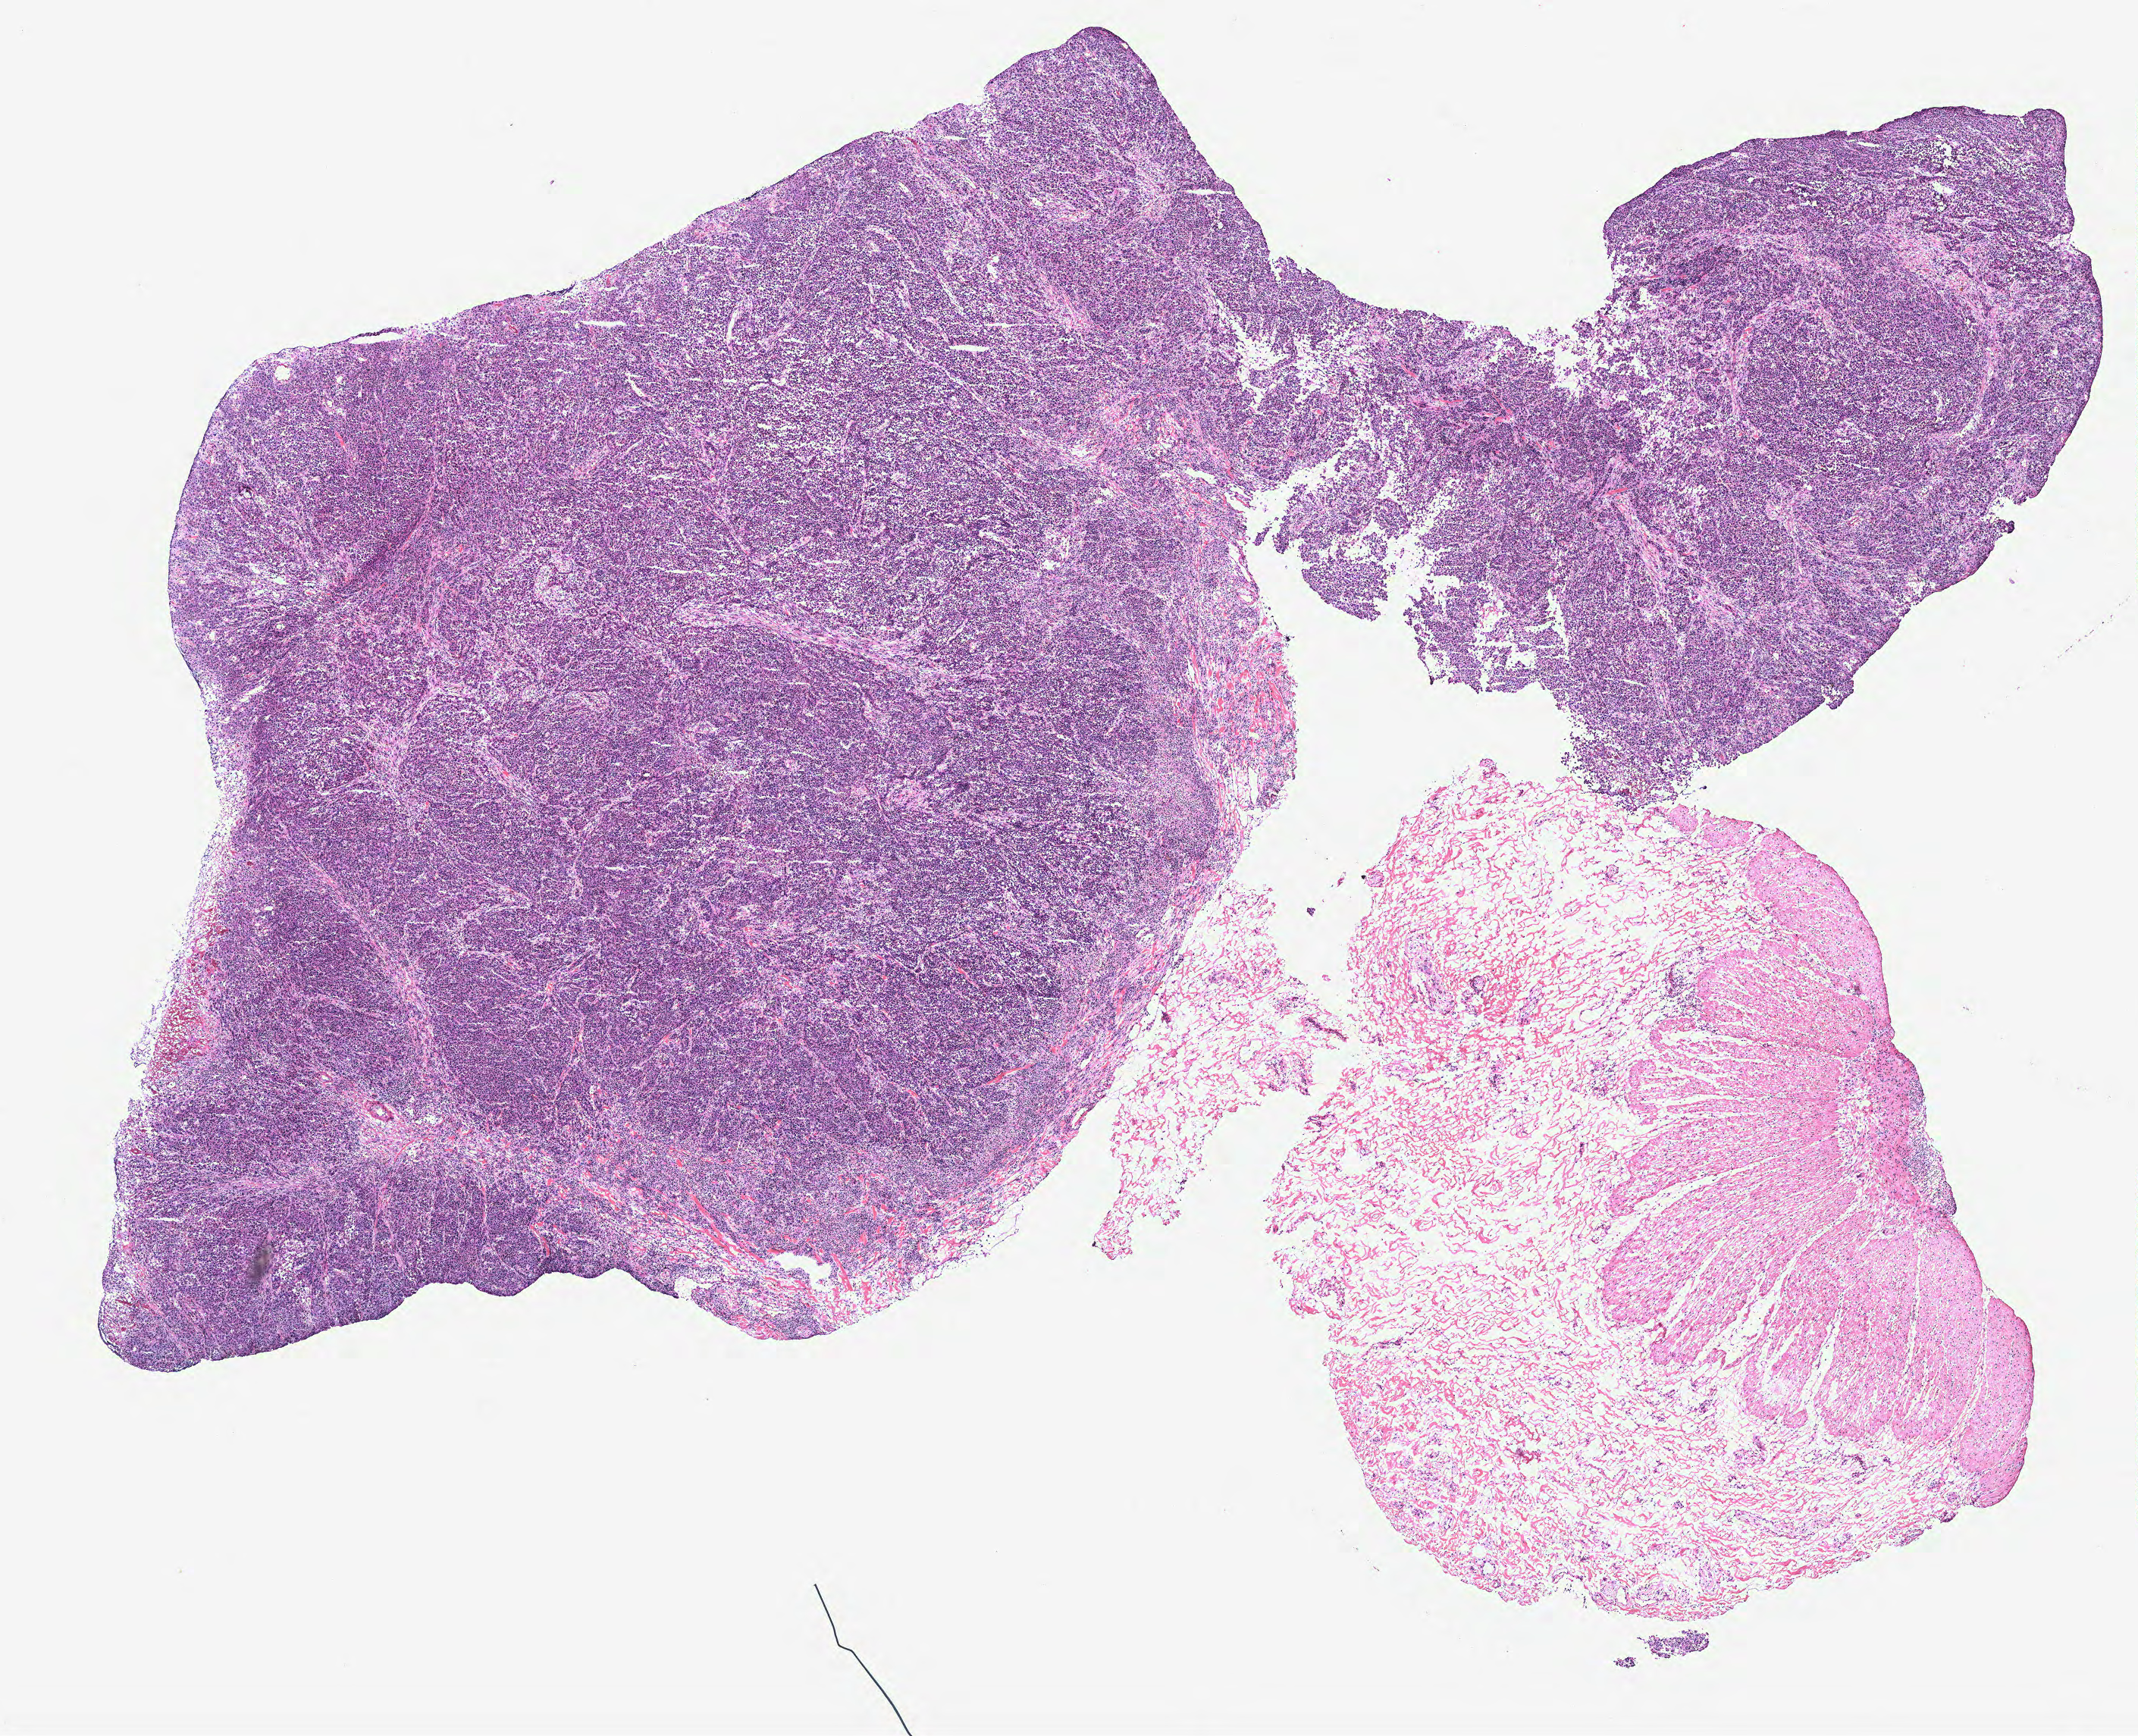
Whole-slide histology image, Hematoxylin and eosin (H&E) stained — a low-resolution overview of the entire scanned area, about 11.3 x 9.2 mm (acquisition: 40x scan). Colon, tissue type not recorded.
- patient diagnosis (cohort enrolment): colon cancer (colon)